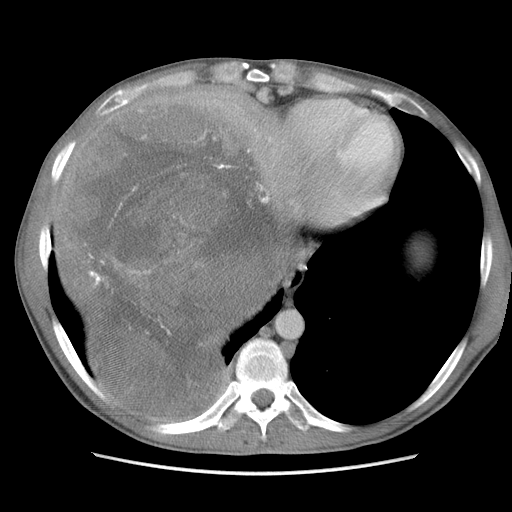
Contrast-enhanced abdominal CT, one axial slice; slice 91 of 115 in the series (ordered by position); soft-tissue window (W 400 / L 40 HU); 5 mm slice thickness; 512 × 512 image matrix, field of view 360 × 360 mm. Male patient. Case-level facts recorded for this patient, not image findings: diagnosis: adrenocortical carcinoma; tumour side: right adrenal; Ki-67 index: 13 %; stage (as recorded): 3.
Annotated regions visible in this slice (semi-automatic segmentation, software-assisted and operator-edited):
- mass: bounding box <64,91,292,415> (left, top, right, bottom; pixels)